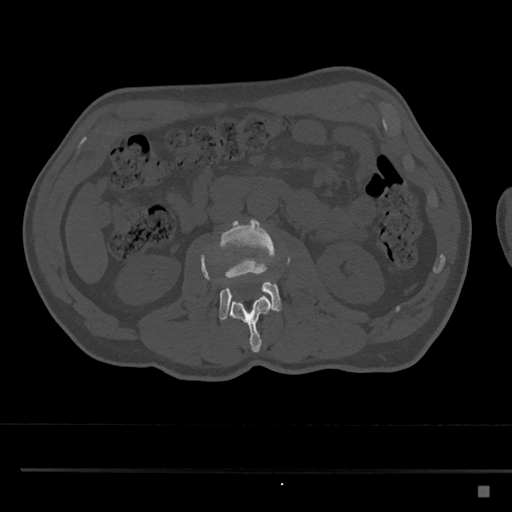
CT including the spine, one axial slice. Bone window (W 1800 / L 400 HU). 0.5 mm slice thickness. 512 × 512 image matrix, field of view 391 × 391 mm. Patient: male, 59 years. Case-level facts recorded for this patient, not image findings: primary cancer: prostate.
Outlined on this slice (semi-automatic segmentation, software-assisted and operator-edited):
- L2 vertebra: bounding box <201,255,273,353> (left, top, right, bottom; pixels)
- L3 vertebra: <201,219,290,320>